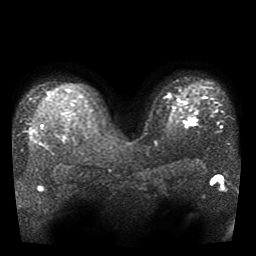
Breast MRI, one axial slice; position 28 of 41 along the scan axis; diffusion-weighted series; image 2 of 4 stored at this slice position (different b-values; order by instance number); 1.5 T; 256 × 256 image matrix, field of view 330 × 330 mm. Female patient.
Annotated regions visible in this slice (manually delineated by an expert):
- tumour on diffusion-weighted imaging: box from (x=190, y=120) to (x=195, y=125) px